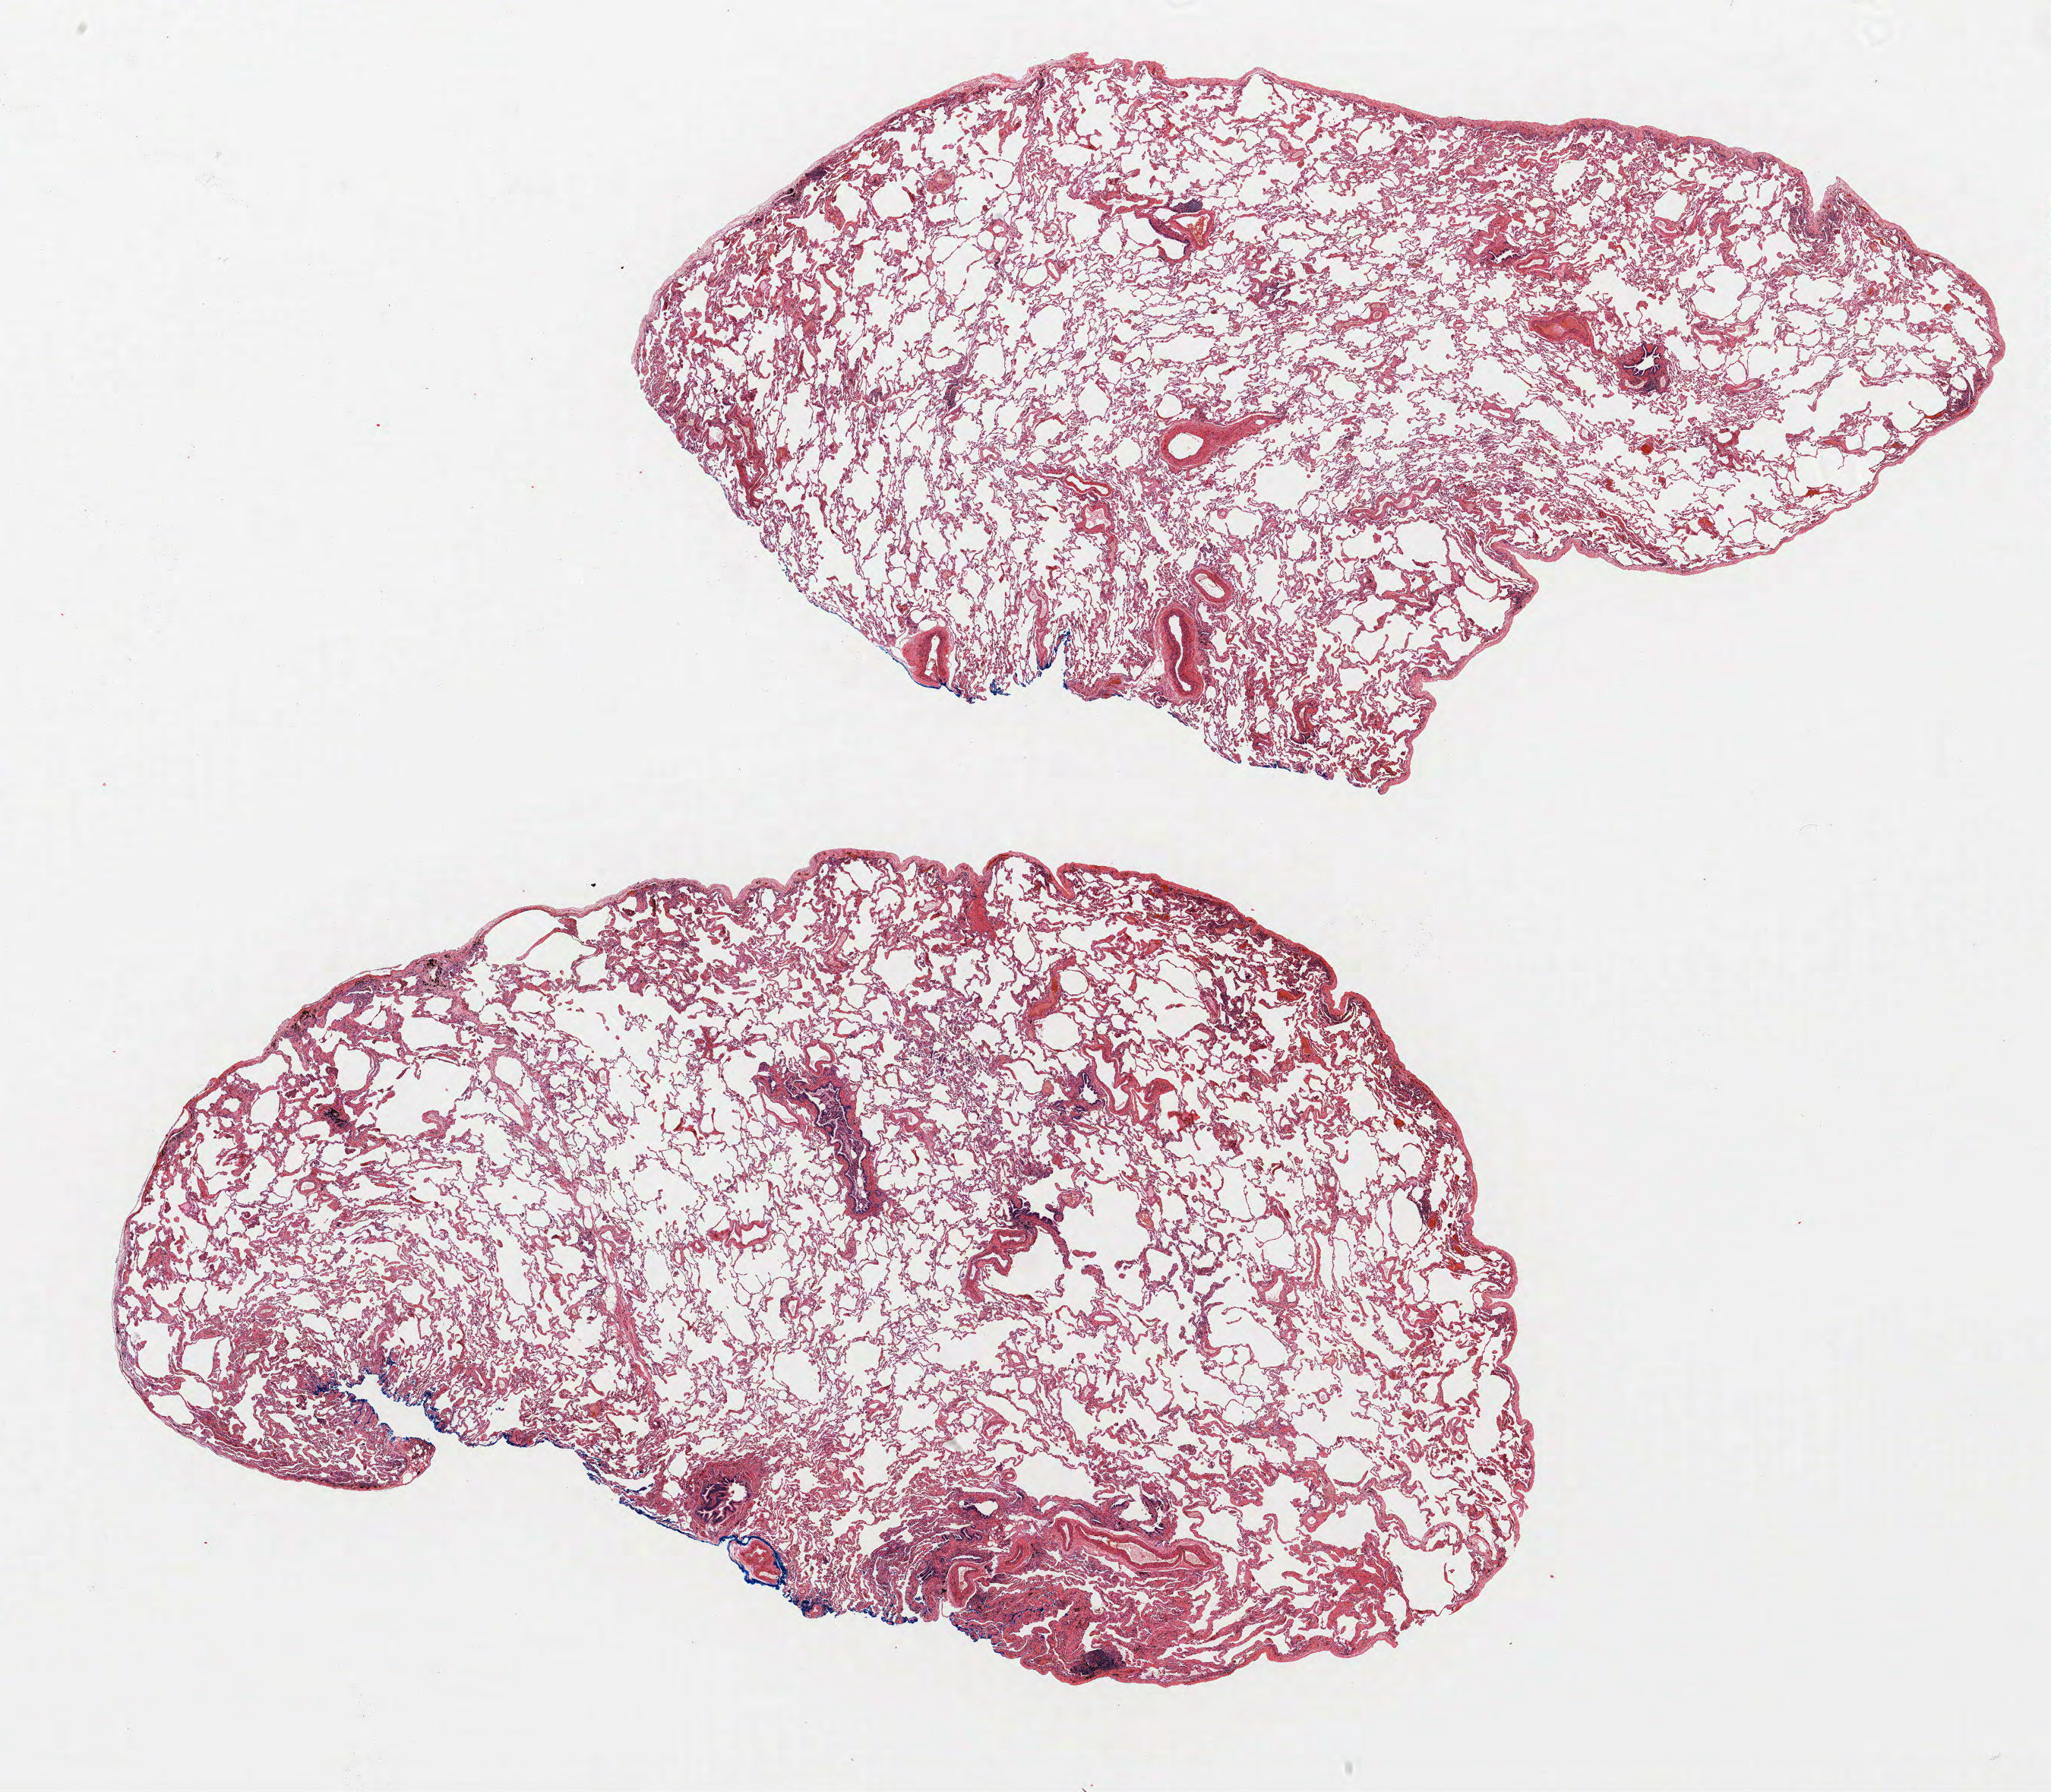
Whole-slide histology image, H&E-stained — whole scanned area (about 21.6 x 18.9 mm) shown as a low-resolution overview. FFPE section. Lung tissue. Female patient, aged 61 at enrolment. Current smoker at enrolment.
Participant's lung-cancer diagnosis: Adenocarcinoma, NOS (ICD-O-3 8140/3).